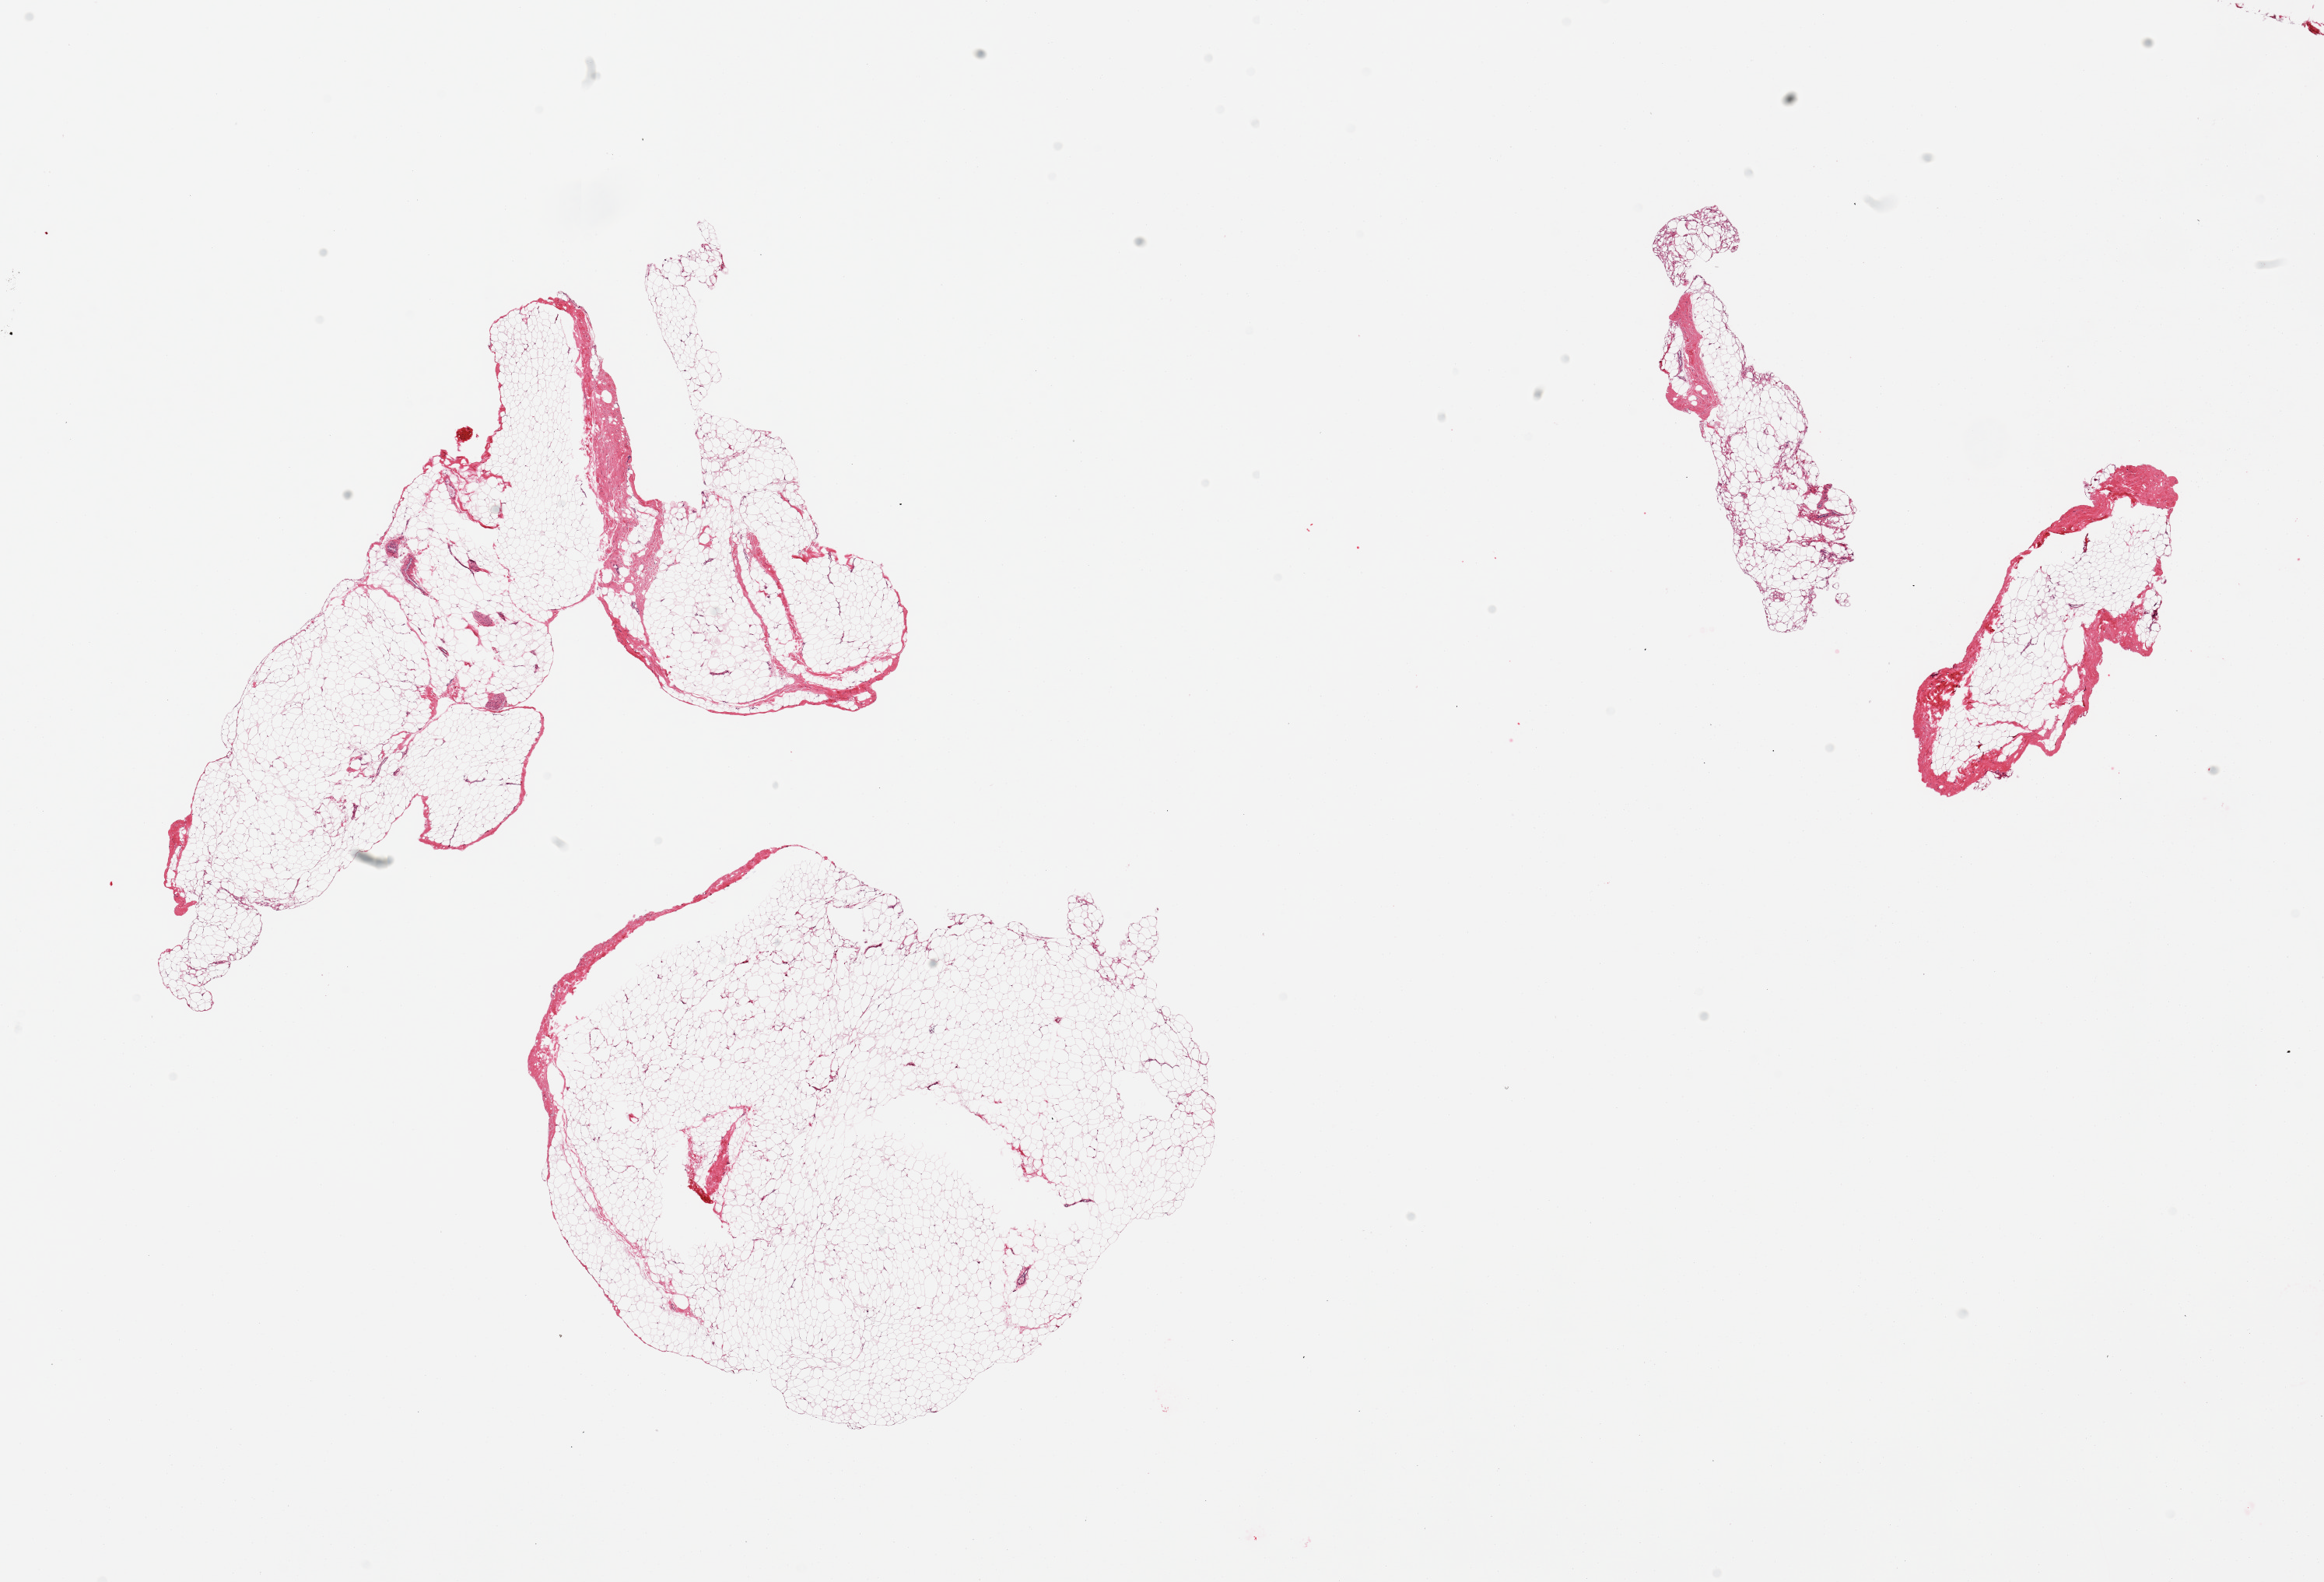
Digitized hematoxylin and eosin (H&E)-stained section, brightfield, whole scanned area (about 23.6 x 16.1 mm, acquisition: 20x scan) shown as a low-resolution overview. PAXgene-fixed, paraffin-embedded tissue. Section of breast (target tissue). Donor tissue sample. Male donor.
* pathologist's review note for this sample: 2 pieces; fibrofatty tissue, no ducts